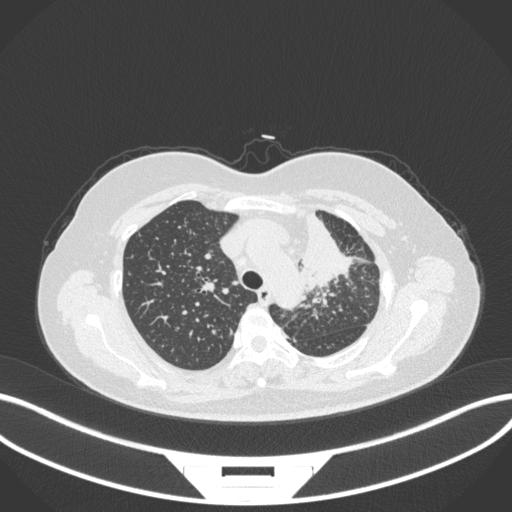
Chest CT, one axial slice. Position 253 of 348 along the scan axis. Reconstruction kernel B31f. 120 kVp. Lung window (W 1500 / L -600 HU). 1 mm slice thickness. 512 × 512 image matrix, field of view 400 × 400 mm. Female patient, age 49 years. Case-level facts recorded for this patient, not image findings: clinical TNM (as recorded): T1c N0 M1.
Outlined on this slice (bounding box drawn by a radiologist):
- lung tumour (recorded histology: adenocarcinoma): bounding box (x1, y1, x2, y2) in pixels: (296, 207, 355, 296)